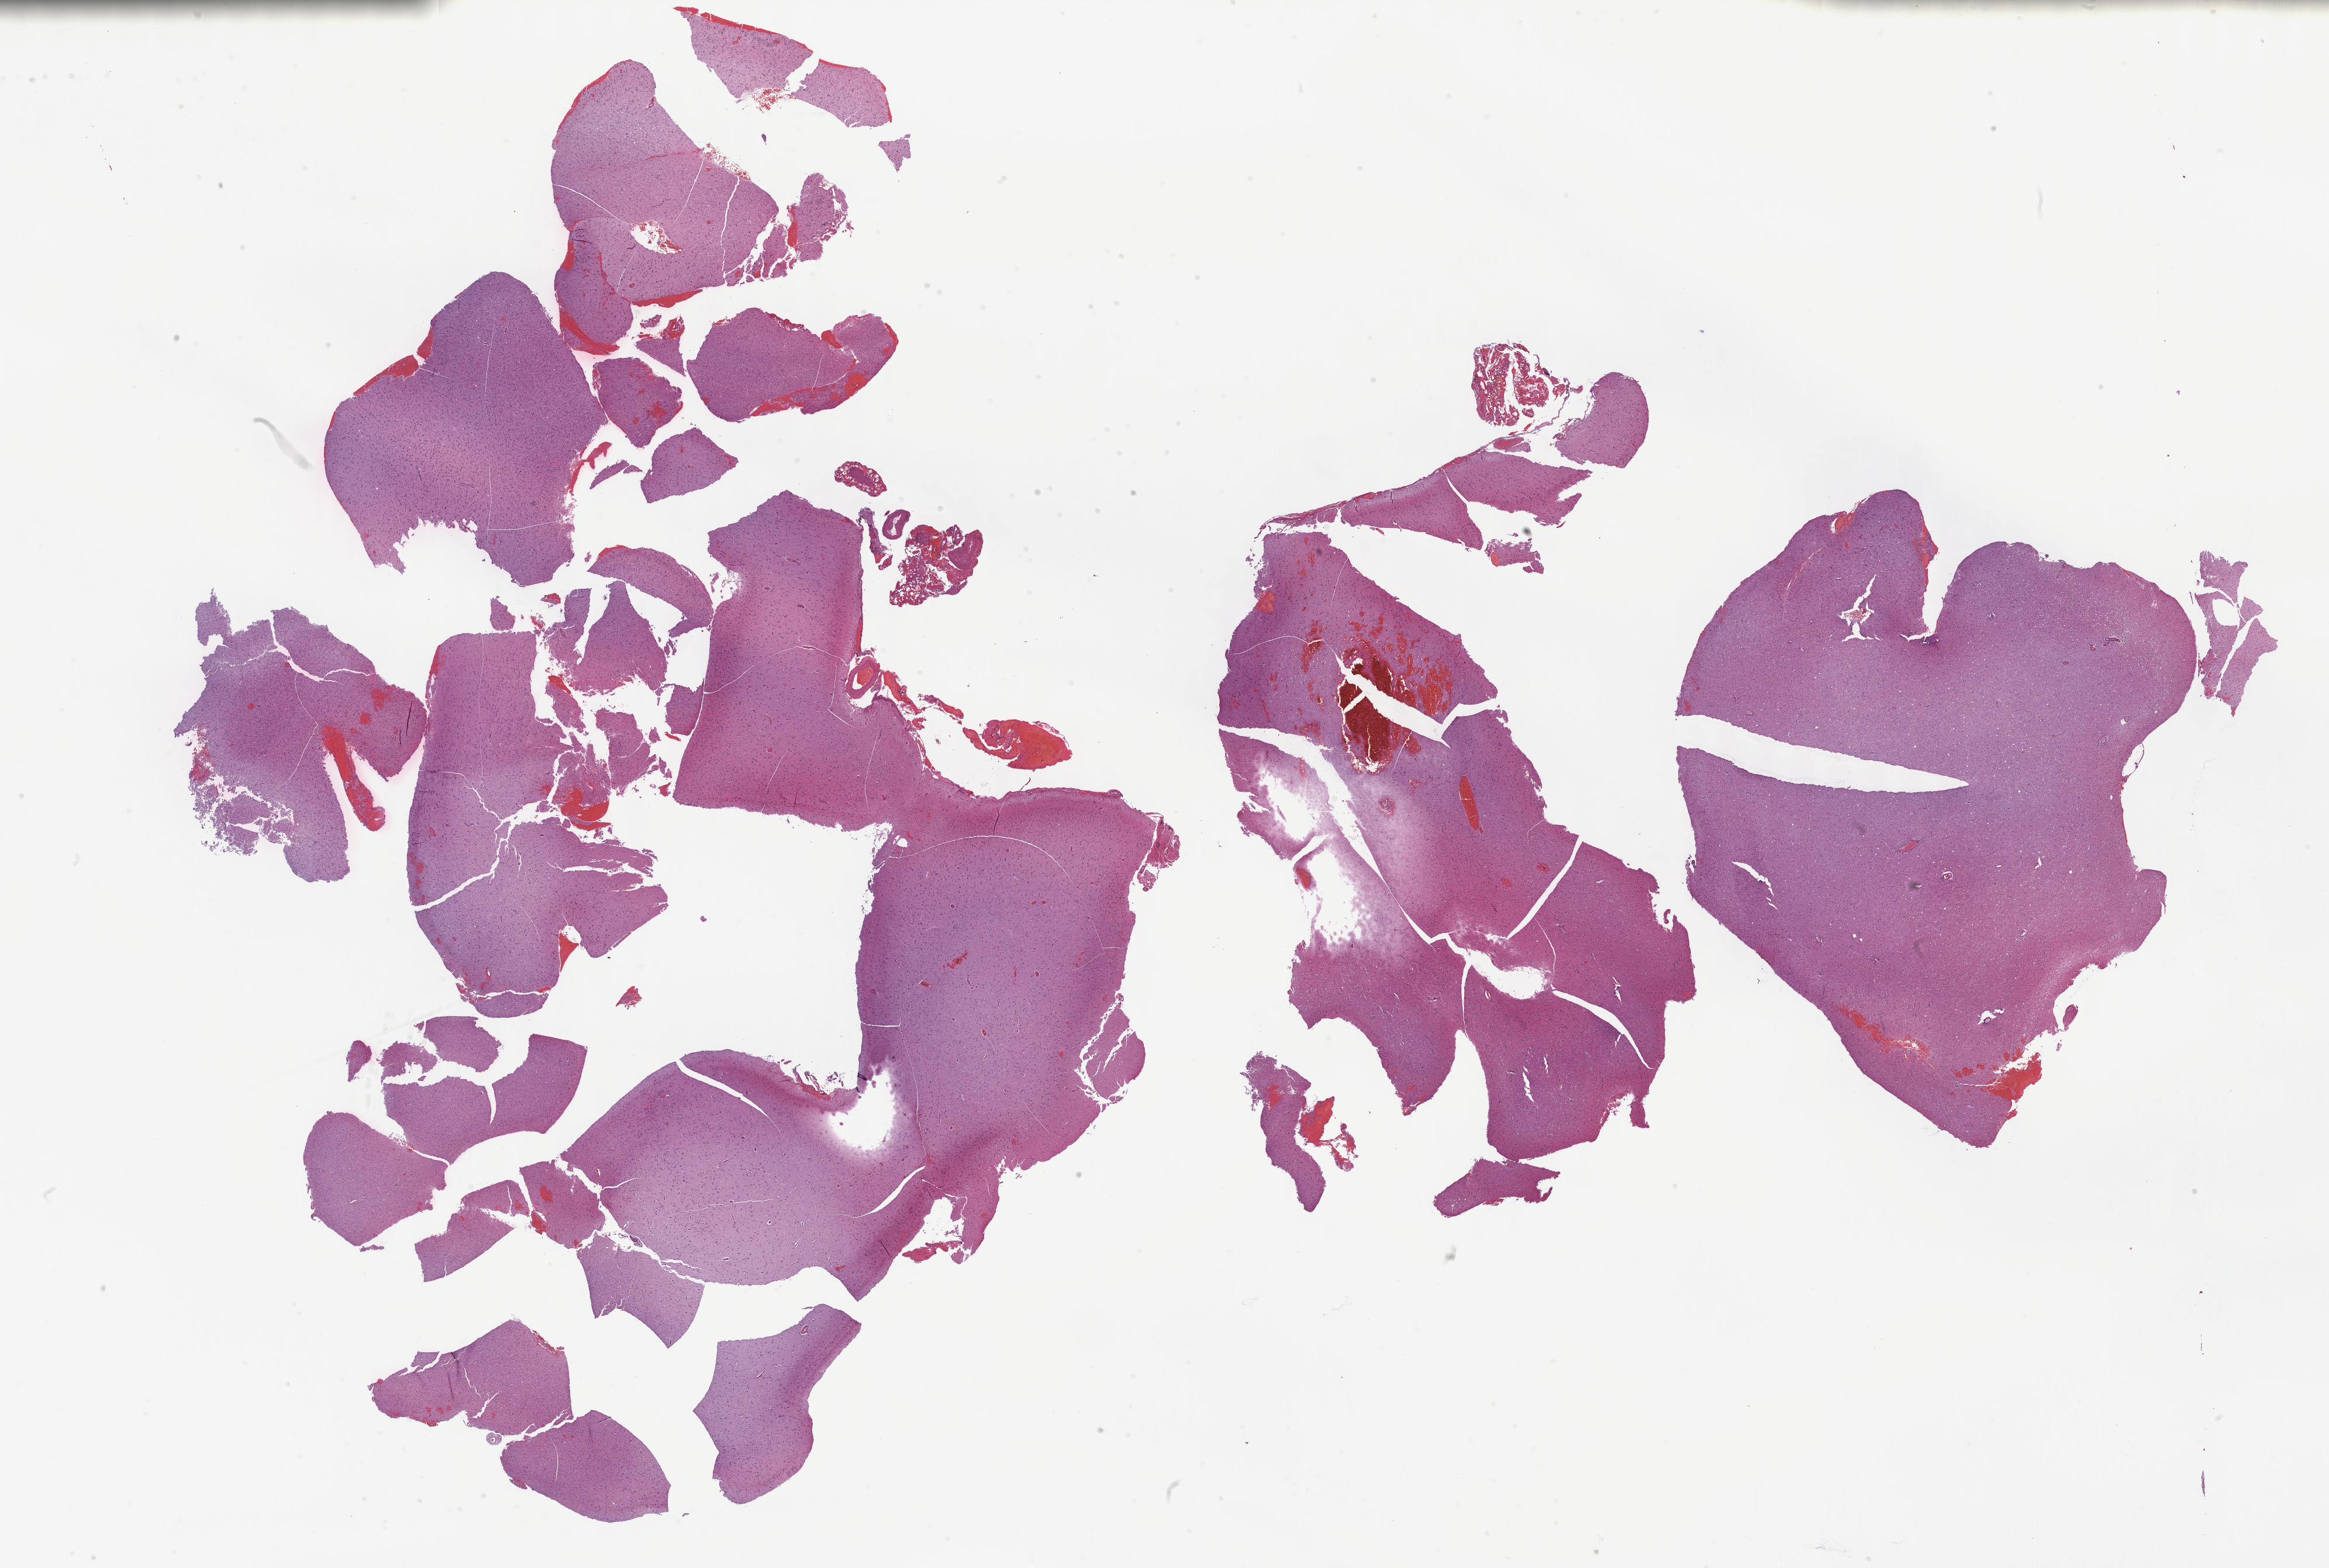
Digitized H&E tissue section (whole slide), low-resolution overview of the scanned area, about 32.2 x 21.7 mm (from a 40x scan). Formalin-fixed paraffin-embedded (FFPE) diagnostic section. Sample: primary tumour, brain. Patient: male, age at initial diagnosis 58 years. Histologic grade: G3 (poorly differentiated).
Diagnosis: Astrocytoma, anaplastic (cerebrum). Laterality: right.